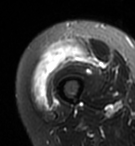
MRI of an extremity soft-tissue mass, one axial slice. Position 19 of 95 along the scan axis. T2-weighted fat-saturated. MR volume resampled by the dataset authors to the PET/CT grid (not the native acquisition matrix). 3.27 mm slice thickness. 135 × 146 image matrix, field of view 132 × 143 mm. Female patient. Case-level facts recorded for this patient, not image findings: histological type: pleiomorphic undifferentiated sarcoma; grade: high; site of the primary tumour: right quadricep.
Annotated regions visible in this slice (expert contour drawn on MRI and transferred to this co-registered scan by the dataset authors):
- gross tumour volume including surrounding oedema: box from (x=32, y=38) to (x=88, y=108) px